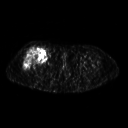
FDG PET of an extremity soft-tissue mass (from a PET/CT study), one axial slice; position 266 of 311 along the scan axis; 3.27 mm slice thickness; 128 × 128 image matrix, field of view 500 × 500 mm. Patient: female, 57 years. Case-level facts recorded for this patient, not image findings: histological type: pleiomorphic undifferentiated sarcoma; grade: high; site of the primary tumour: right quadricep.
Annotated regions visible in this slice (expert contour drawn on MRI and transferred to this co-registered scan by the dataset authors):
- tumour plus oedema (research contour): bounding box [x1, y1, x2, y2] px = [23, 47, 47, 70]
- tumour (research contour): [23, 47, 47, 70]